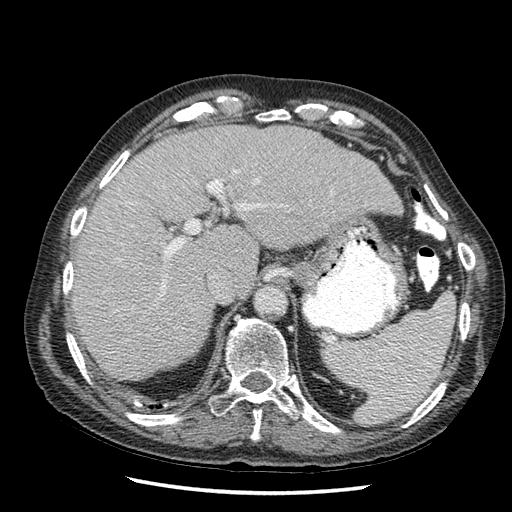
Contrast-enhanced abdominal CT (liver protocol), one axial slice. Position 38 of 67 along the scan axis. Reconstruction kernel STANDARD. 120 kVp. Soft-tissue window (W 400 / L 40 HU). 2.5 mm slice thickness. 512 × 512 image matrix. From the clinical record (not read from this slice): diagnosis: hepatocellular carcinoma (patient treated with transarterial chemoembolisation; whether this scan precedes or follows treatment is not stated here); TNM stage (as recorded): Stage-I; Child-Pugh class: A.
Annotated regions visible in this slice (semi-automatically segmented with operator editing):
- liver parenchyma outside the tumour (the mass and vessels are separate outlines, so this box may not span the whole liver): bounding box [x1, y1, x2, y2] px = [70, 124, 402, 380]
- liver vessels: [74, 169, 289, 309]